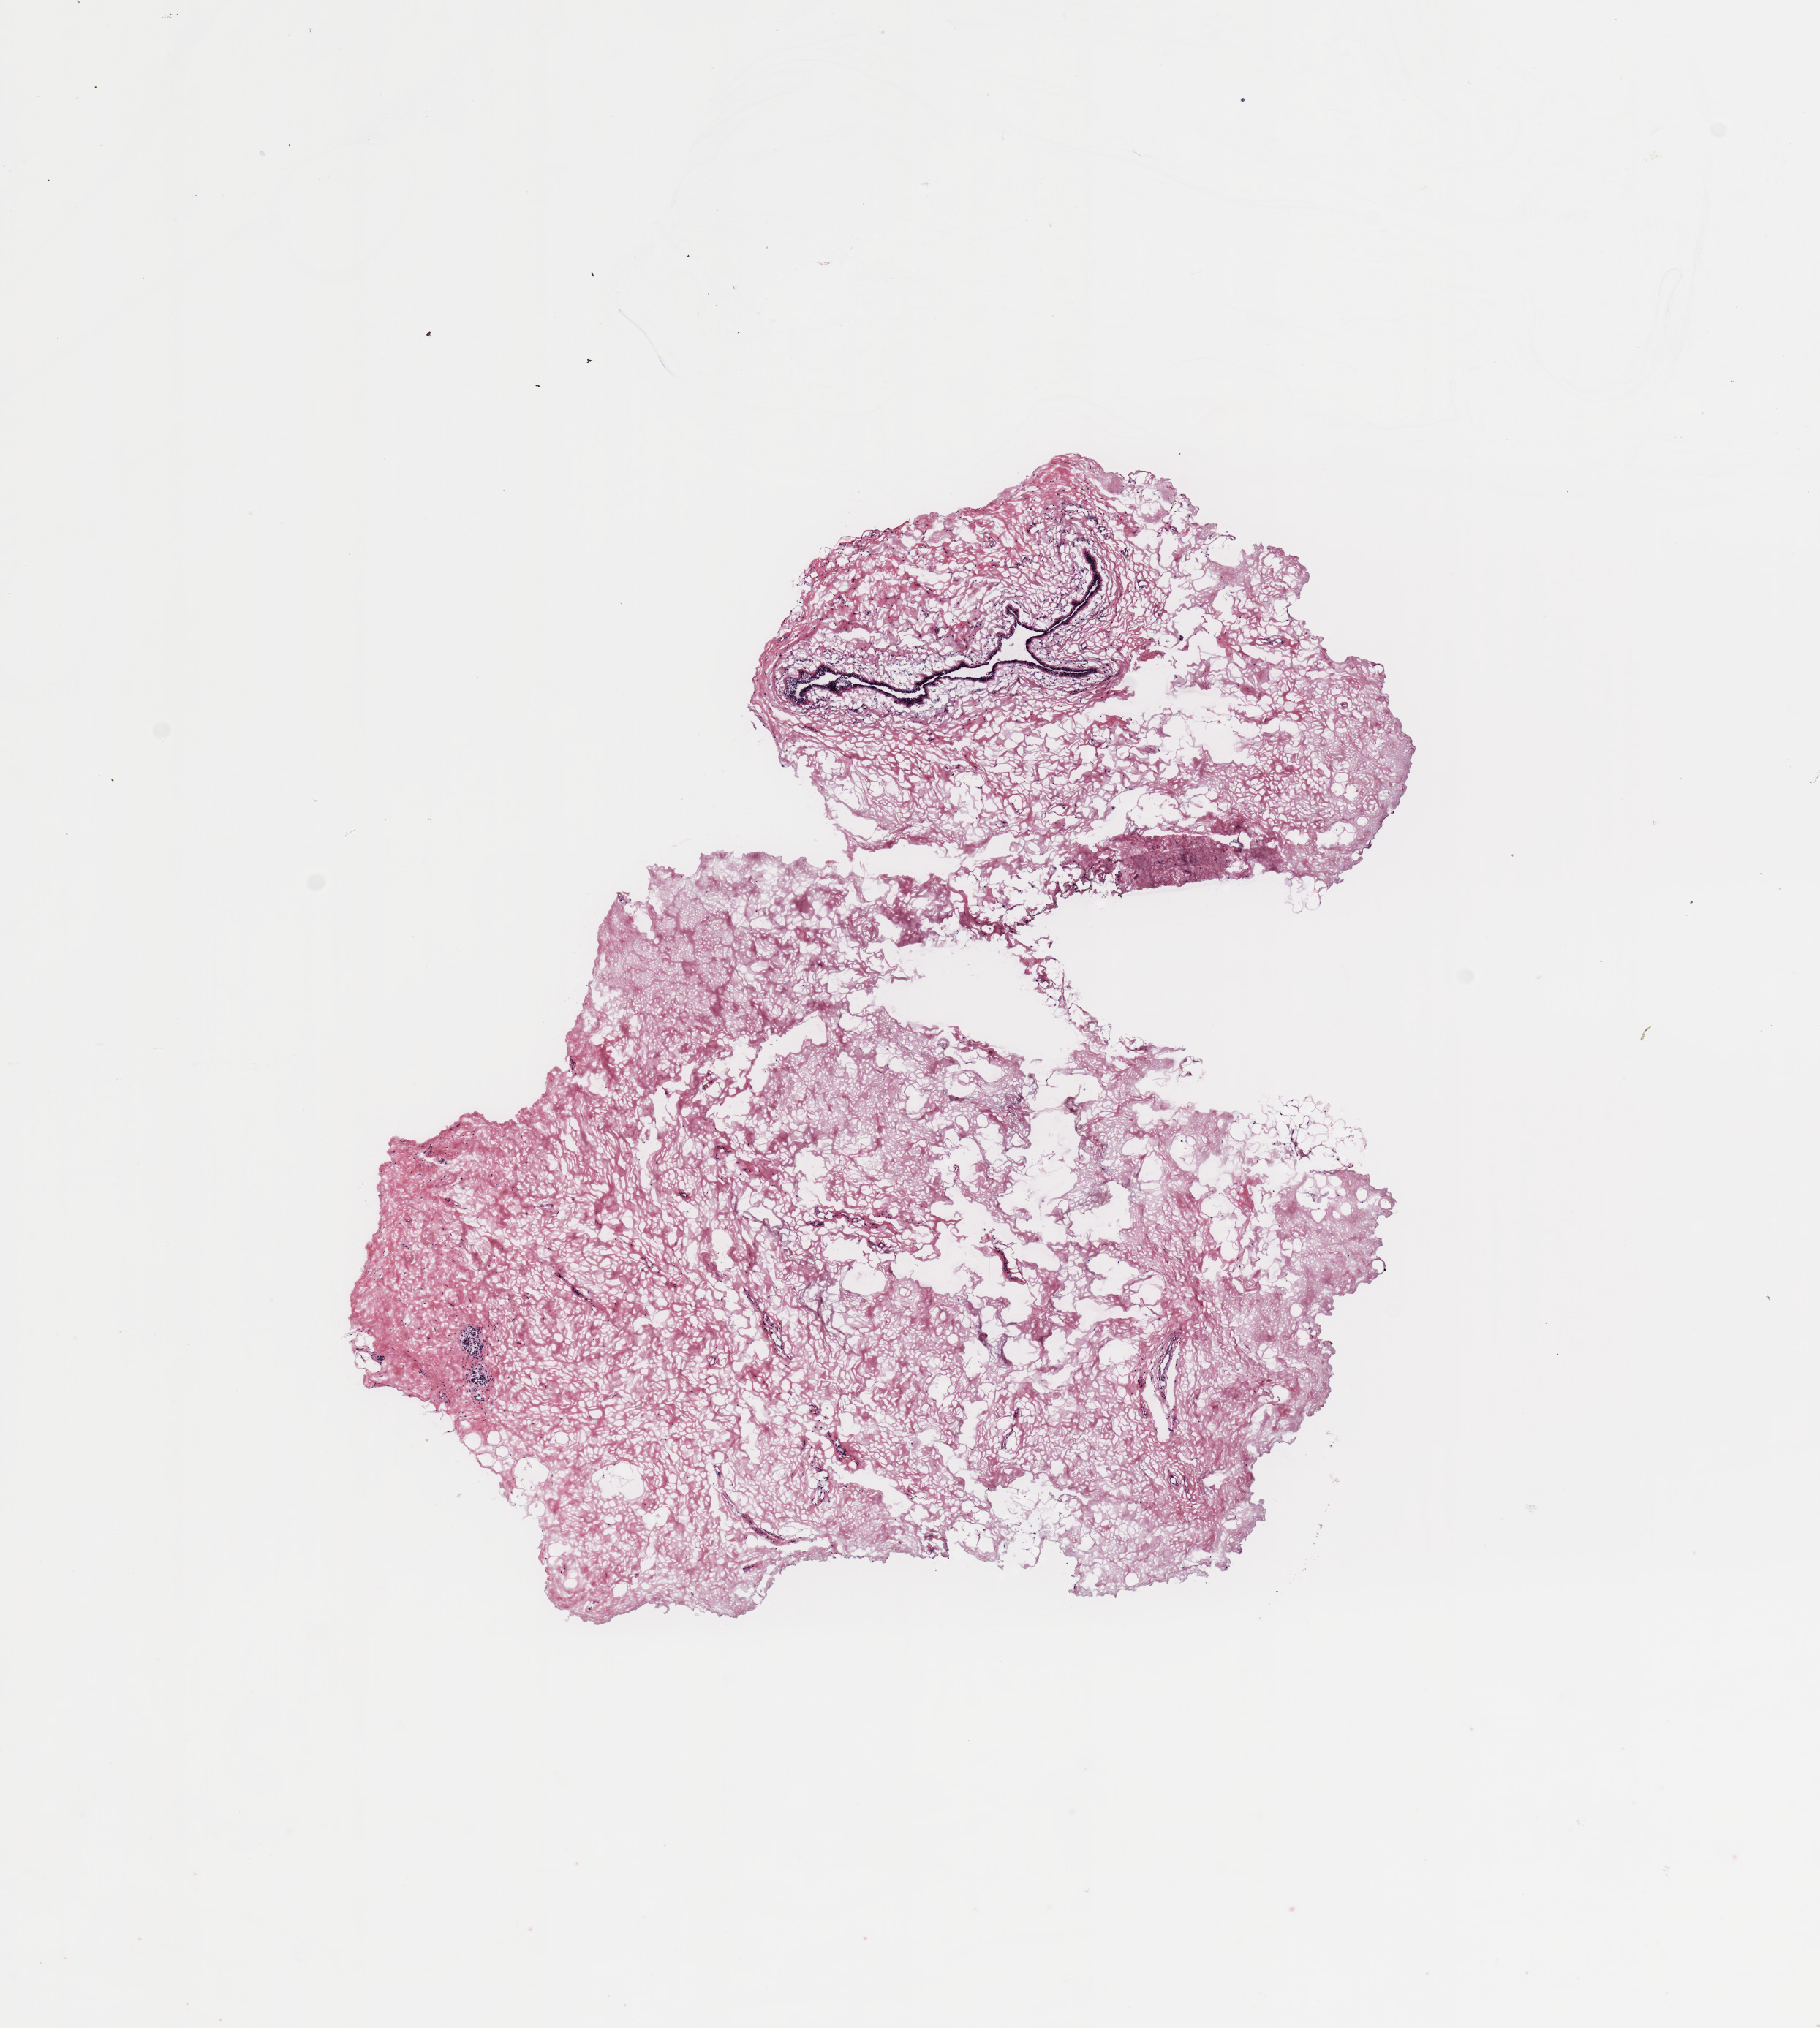
Digitized H&E-stained tissue section (whole slide) — low-resolution overview of the scanned area, about 9.8 x 11.0 mm. Breast, tumour tissue. Female, 61 y/o.
- histologic diagnosis: Infiltrating duct carcinoma, NOS
- AJCC pathologic stage: IIA